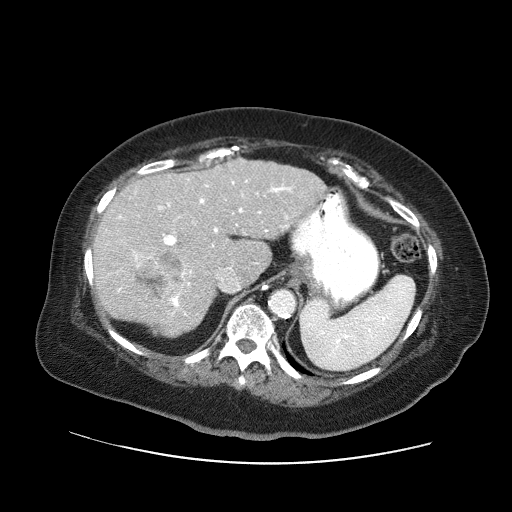
Contrast-enhanced abdominal CT (liver protocol), one axial slice; position 38 of 71 along the scan axis; reconstruction kernel STANDARD; soft-tissue window (W 400 / L 40 HU); 2.5 mm slice thickness; 512 × 512 image matrix, field of view 400 × 400 mm. From the clinical record (not read from this slice): diagnosis: hepatocellular carcinoma (patient treated with transarterial chemoembolisation; whether this scan precedes or follows treatment is not stated here); TNM stage (as recorded): Stage-II; Child-Pugh class: A; tumour differentiation: poorly differentiated; tumour size: 5 cm.
Annotated regions visible in this slice (semi-automatically segmented with operator editing):
- liver parenchyma outside the tumour (the mass and vessels are separate outlines, so this box may not span the whole liver): bounding box (x1, y1, x2, y2) in pixels: (92, 158, 325, 336)
- mass: (135, 250, 185, 302)
- liver vessels: (117, 180, 292, 315)